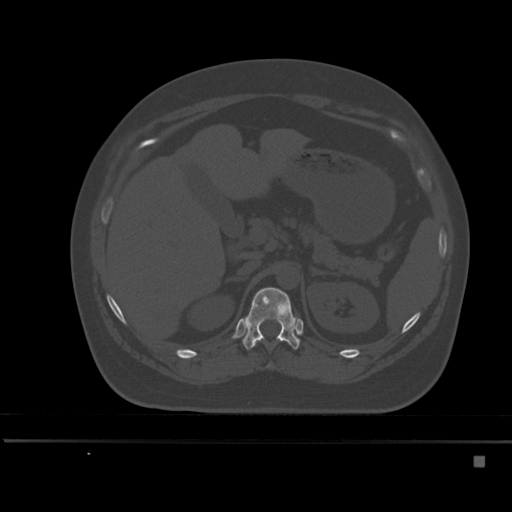
CT including the spine, one axial slice. Position 217 of 495 along the scan axis. Bone window (W 1800 / L 400 HU). 512 × 512 image matrix, field of view 404 × 404 mm. Female patient, age 33 years. From the clinical record (not read from this slice): primary cancer: breast; vertebrae with lytic lesions (as recorded): T1.
Annotated regions visible in this slice (semi-automatically segmented with operator editing):
- T11 vertebra: box from (x=268, y=365) to (x=270, y=367) px
- T12 vertebra: (x=242, y=287)–(x=300, y=350)